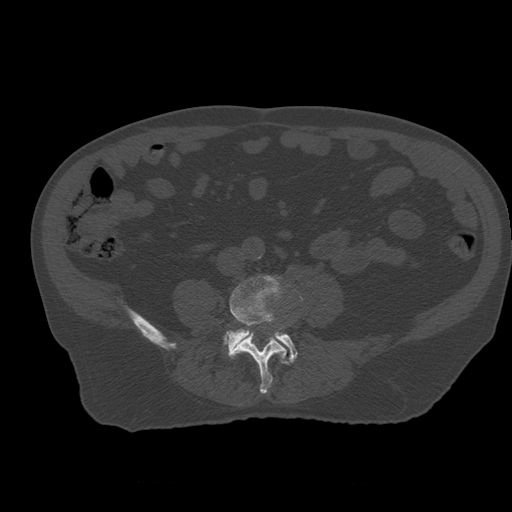
CT including the spine, one axial slice; position 157 of 399 along the scan axis; reconstruction kernel STANDARD; bone window (W 1800 / L 400 HU); 512 × 512 image matrix, field of view 407 × 407 mm. Patient age 73 years. From the clinical record (not read from this slice): primary cancer: prostate; vertebrae with lytic lesions (as recorded): L2.
Annotated regions visible in this slice (semi-automatic segmentation, software-assisted and operator-edited):
- L4 vertebra: bounding box [x1, y1, x2, y2] px = [223, 276, 287, 394]
- L5 vertebra: [228, 329, 298, 364]